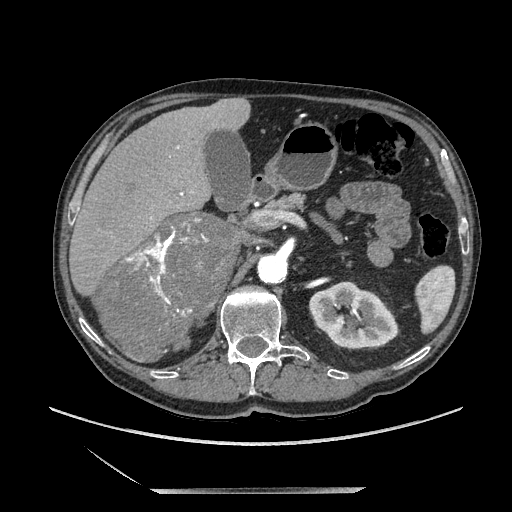
Contrast-enhanced abdominal CT, one axial slice. Slice 122 of 243 in the series (ordered by position). Soft-tissue window (W 400 / L 40 HU). 1.25 mm slice thickness. 512 × 512 image matrix. Male patient. Case-level facts recorded for this patient, not image findings: diagnosis: adrenocortical carcinoma; tumour side: right adrenal; tumour size at pathology: 16 cm; Ki-67 index: 17 %; stage (as recorded): 3.
Structures marked on this image (semi-automatic segmentation, software-assisted and operator-edited):
- mass: bounding box [x1, y1, x2, y2] px = [99, 214, 238, 362]